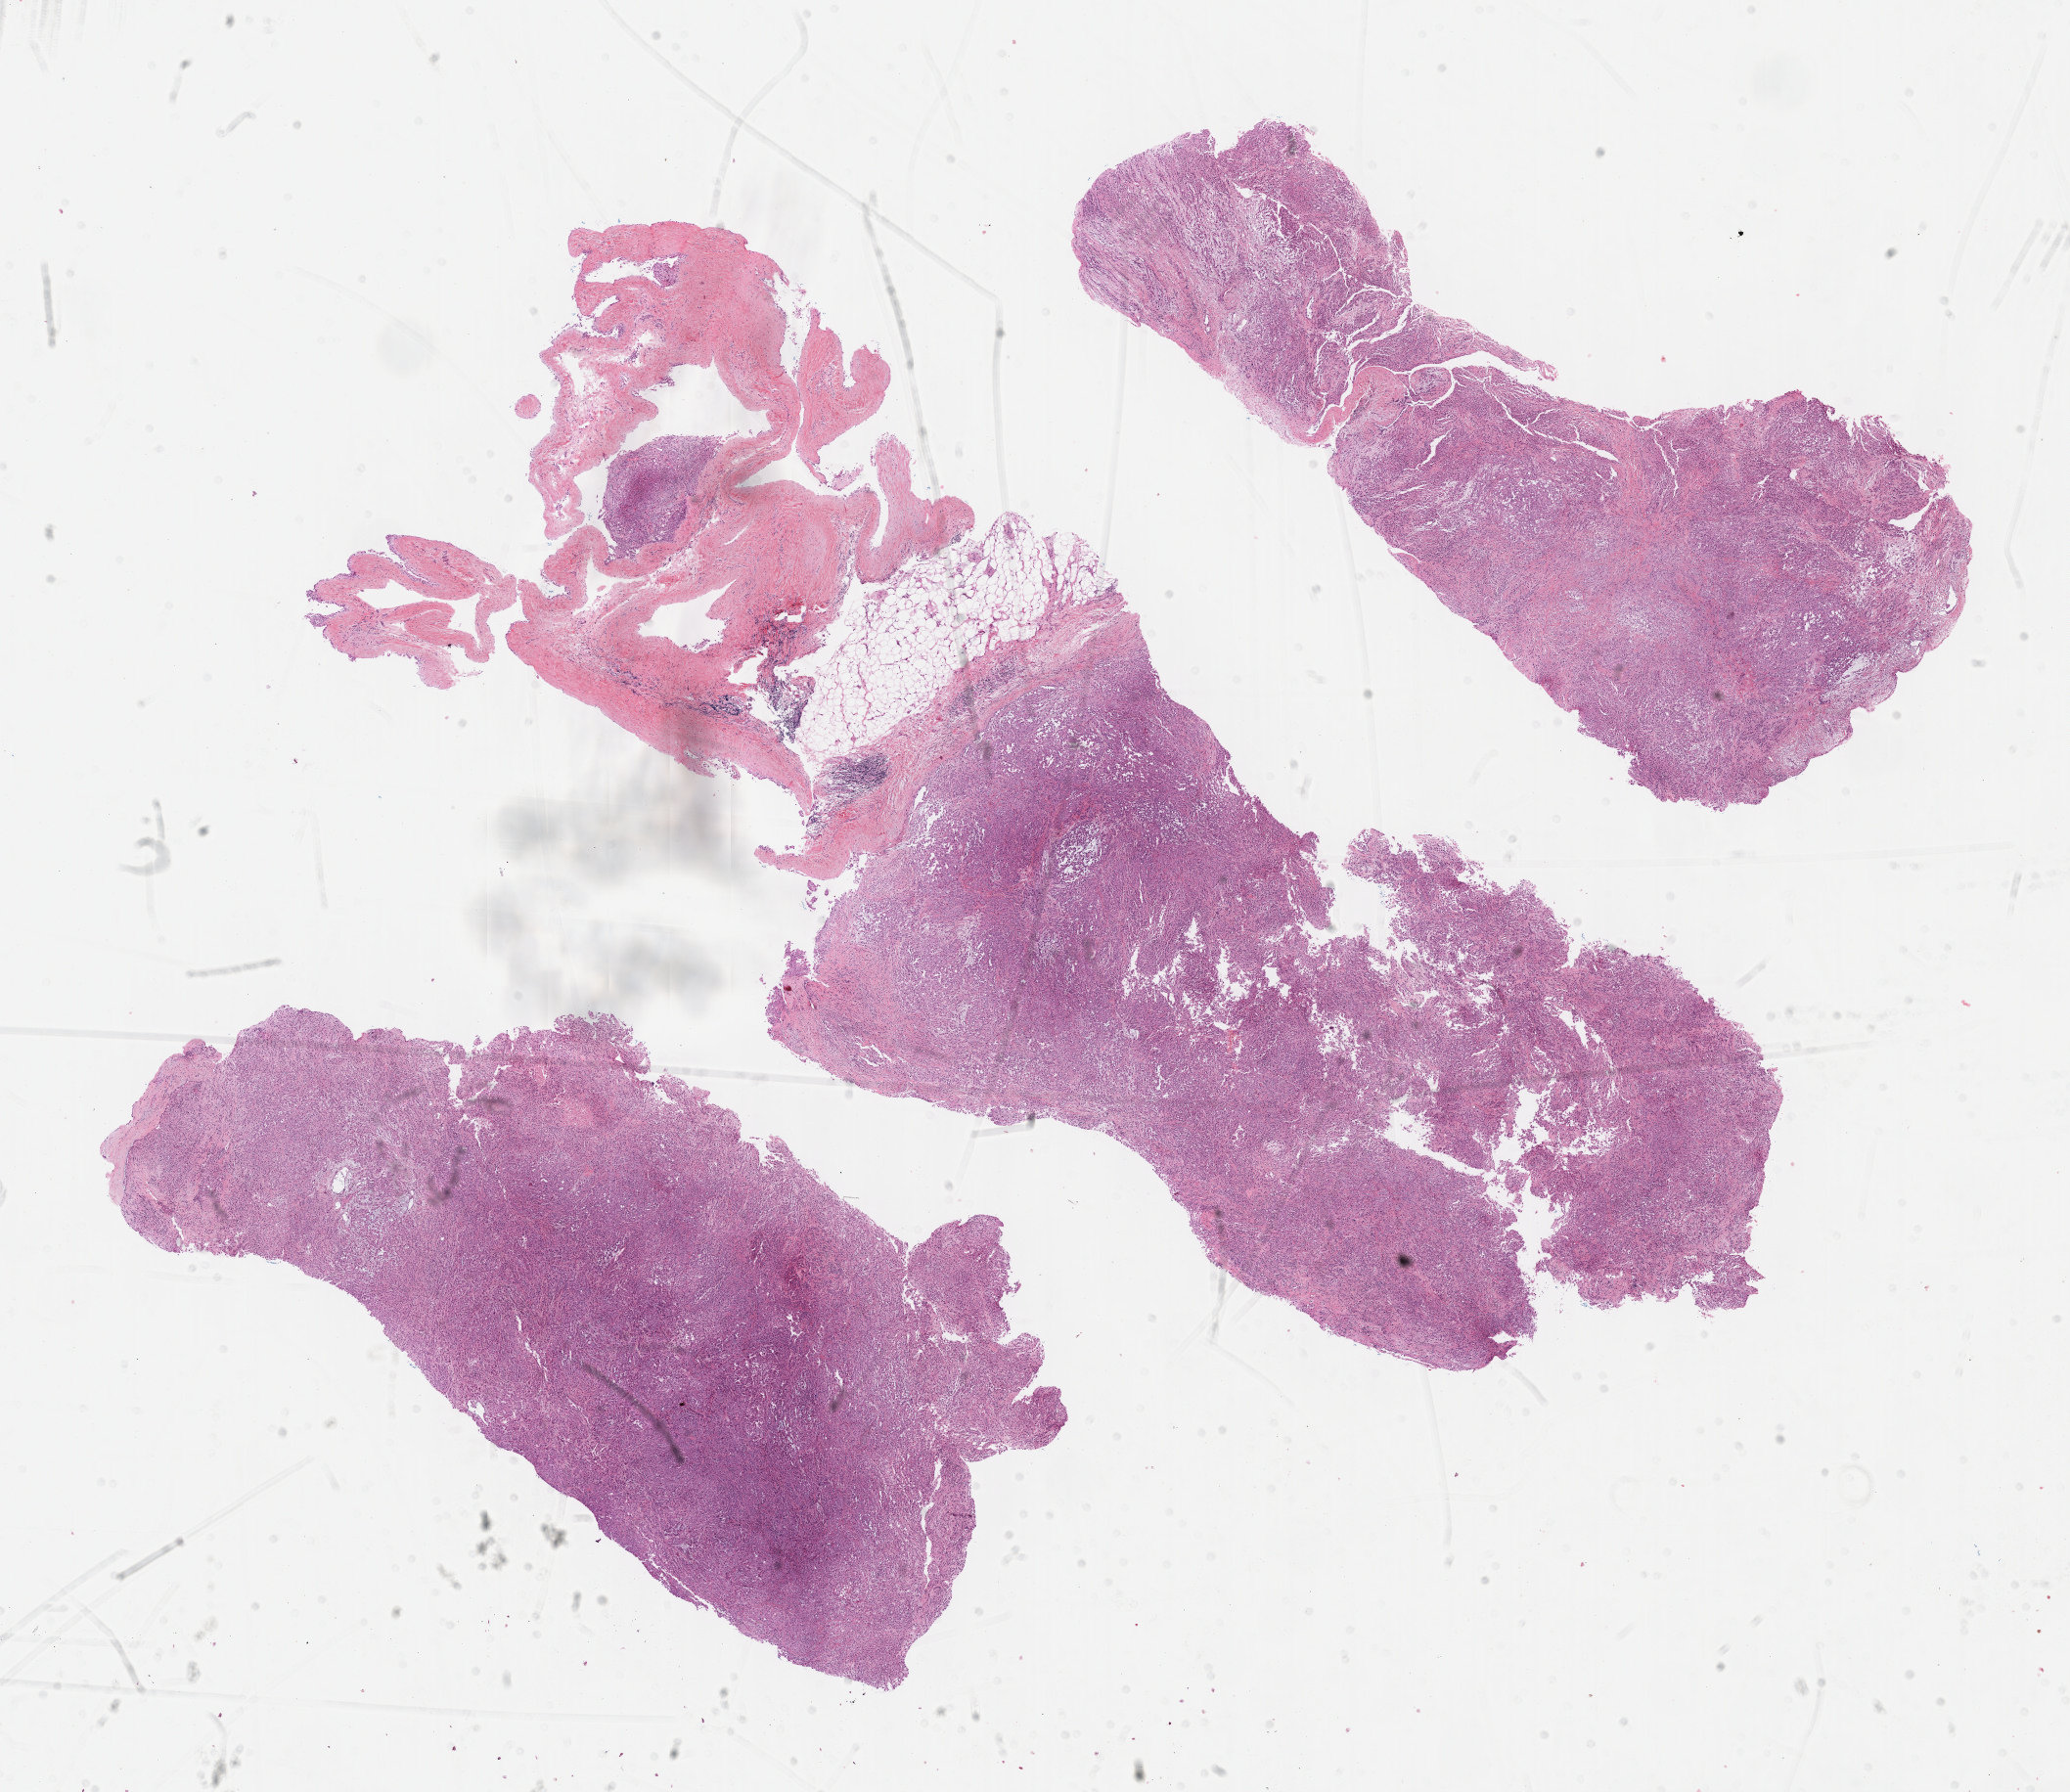
Hematoxylin and eosin (H&E) stained whole-slide image, low-resolution overview of the scanned area, about 17.1 x 14.8 mm; formalin-fixed paraffin-embedded (FFPE) diagnostic section; primary tumour sample from the mesothelium. Male, age 74 years at initial diagnosis.
- TNM: T1 N0 M0
- pathologic diagnosis: Epithelioid mesothelioma, malignant (pleura, NOS)
- AJCC pathologic stage: I (7th edition)
- laterality: right